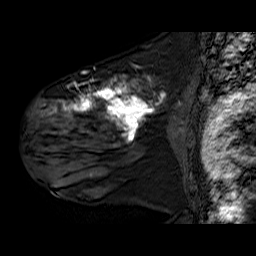
Breast MRI (dynamic contrast-enhanced), one sagittal slice. Position 41 of 60 along the scan axis. Dynamic contrast-enhanced series, time point 2 of 6 at this slice position (early post-contrast). 1.5 T. TE 6.3 ms, TR 32.9 ms. 4 mm slice thickness. 256 × 256 image matrix, field of view 200 × 200 mm. Female patient. Case-level facts recorded for this patient, not image findings: setting: breast cancer imaged before/during neoadjuvant chemotherapy; receptor status: HER2-positive.
Structures marked on this image (semi-automatically segmented with operator editing):
- analysis volume of interest (the breast-tissue region the enhancement analysis was run in; not a lesion): bounding box (x1, y1, x2, y2) in pixels: (30, 78, 178, 180)
- tumour enhancement mask (voxels above the 100 % enhancement threshold inside the analysis volume of interest): (50, 78, 166, 177)